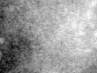
Crop from a digitized film mammogram around one marked abnormality; right breast; MLO view; BI-RADS breast density category 3 (scale 1–4).
- Marked abnormality: calcifications, morphology pleomorphic, distribution clustered; BI-RADS assessment category 4; subtlety rating 3 on a 1 (subtle) to 5 (obvious) scale; pathology result (as recorded, not read from the image): malignant.